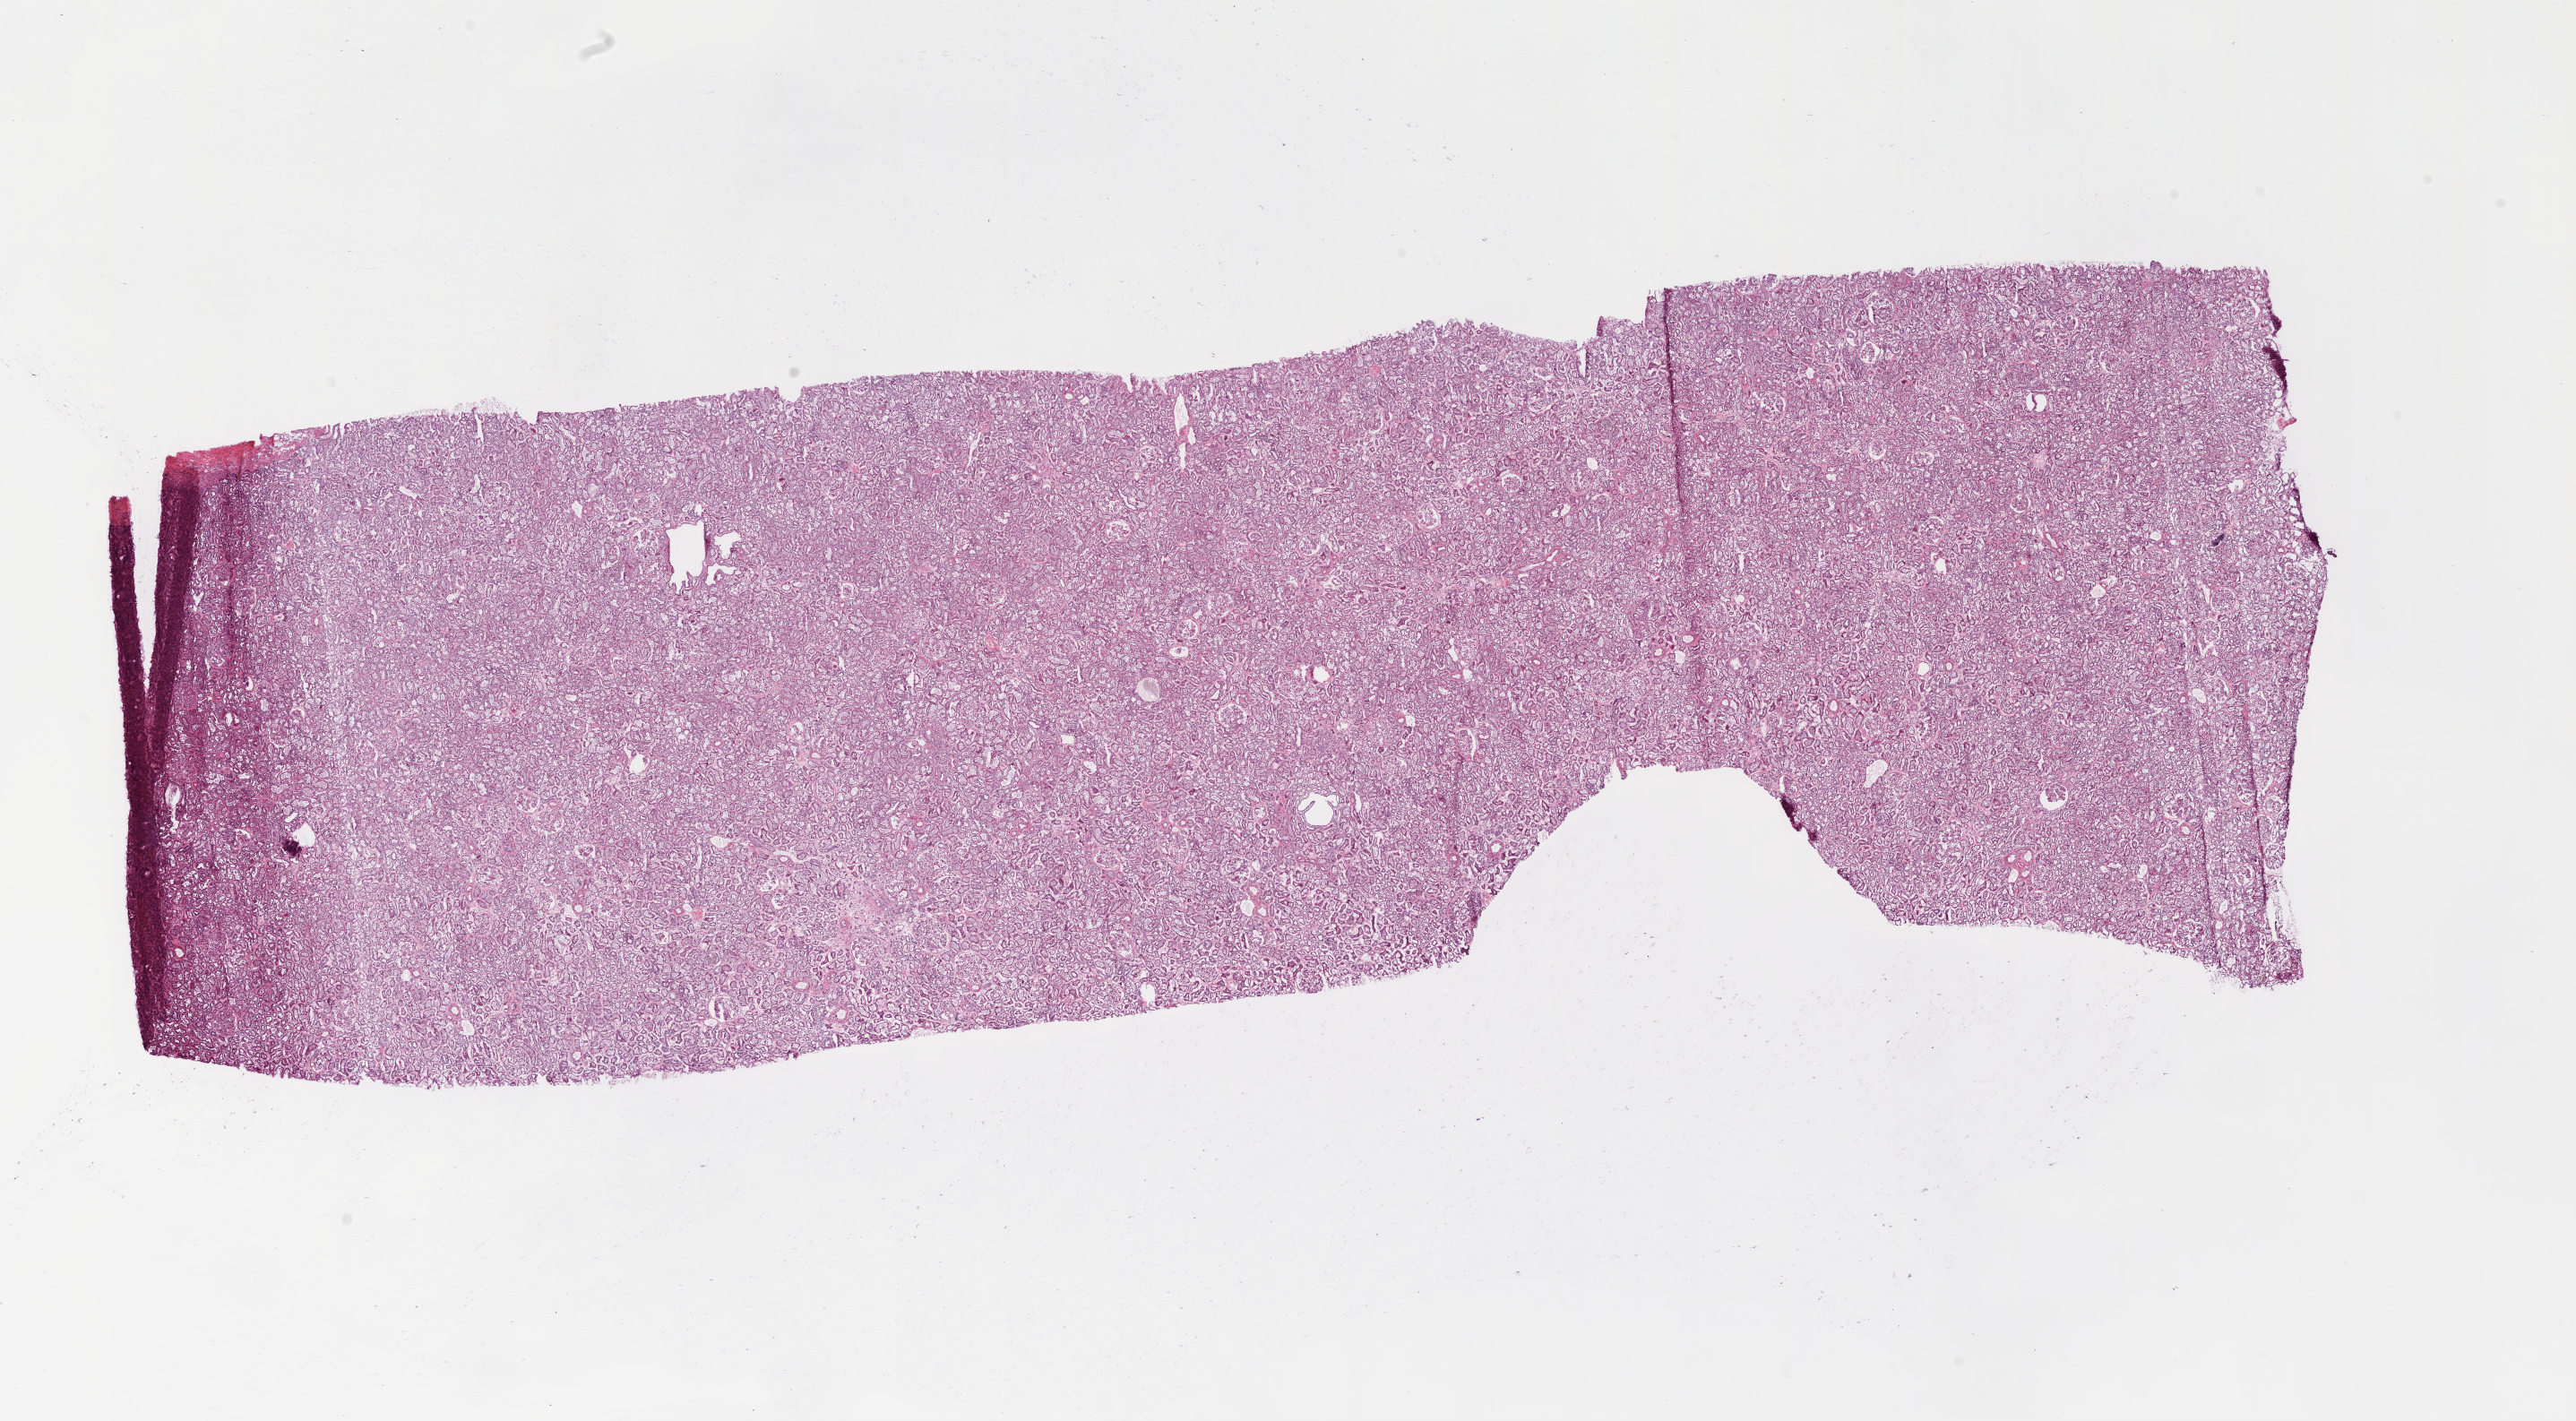
Digitized Hematoxylin and eosin (H&E) stained tissue section (whole slide) — shown as a low-resolution overview of the whole scanned area (about 23.1 x 12.7 mm, slide scanned at 20x), frozen section, solid tissue normal (non-tumour tissue) sample from the kidney. Male, age 59 years at initial diagnosis.
This section: solid tissue normal (non-tumour) sample from the same patient. Patient diagnosis: Clear cell adenocarcinoma, NOS.